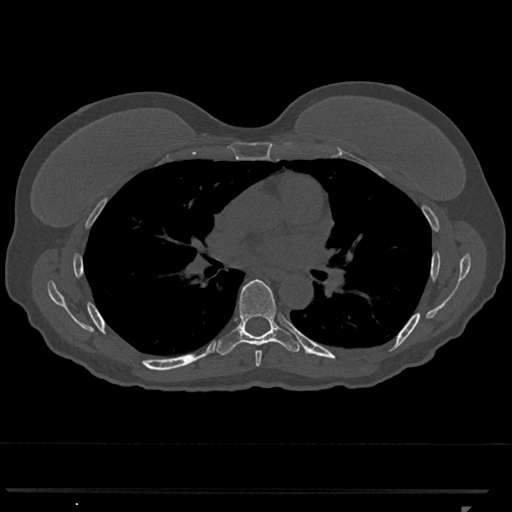
CT including the spine, one axial slice. Slice 723 of 793 in the series (ordered by position). 120 kVp. Bone window (W 1800 / L 400 HU). 0.5 mm slice thickness. 512 × 512 image matrix, field of view 380 × 380 mm. Female patient, age 62 years. From the clinical record (not read from this slice): primary cancer: renal.
Annotated regions visible in this slice (semi-automatically segmented with operator editing):
- T6 vertebra: bounding box [x1, y1, x2, y2] px = [255, 350, 262, 367]
- T7 vertebra: [215, 279, 302, 356]